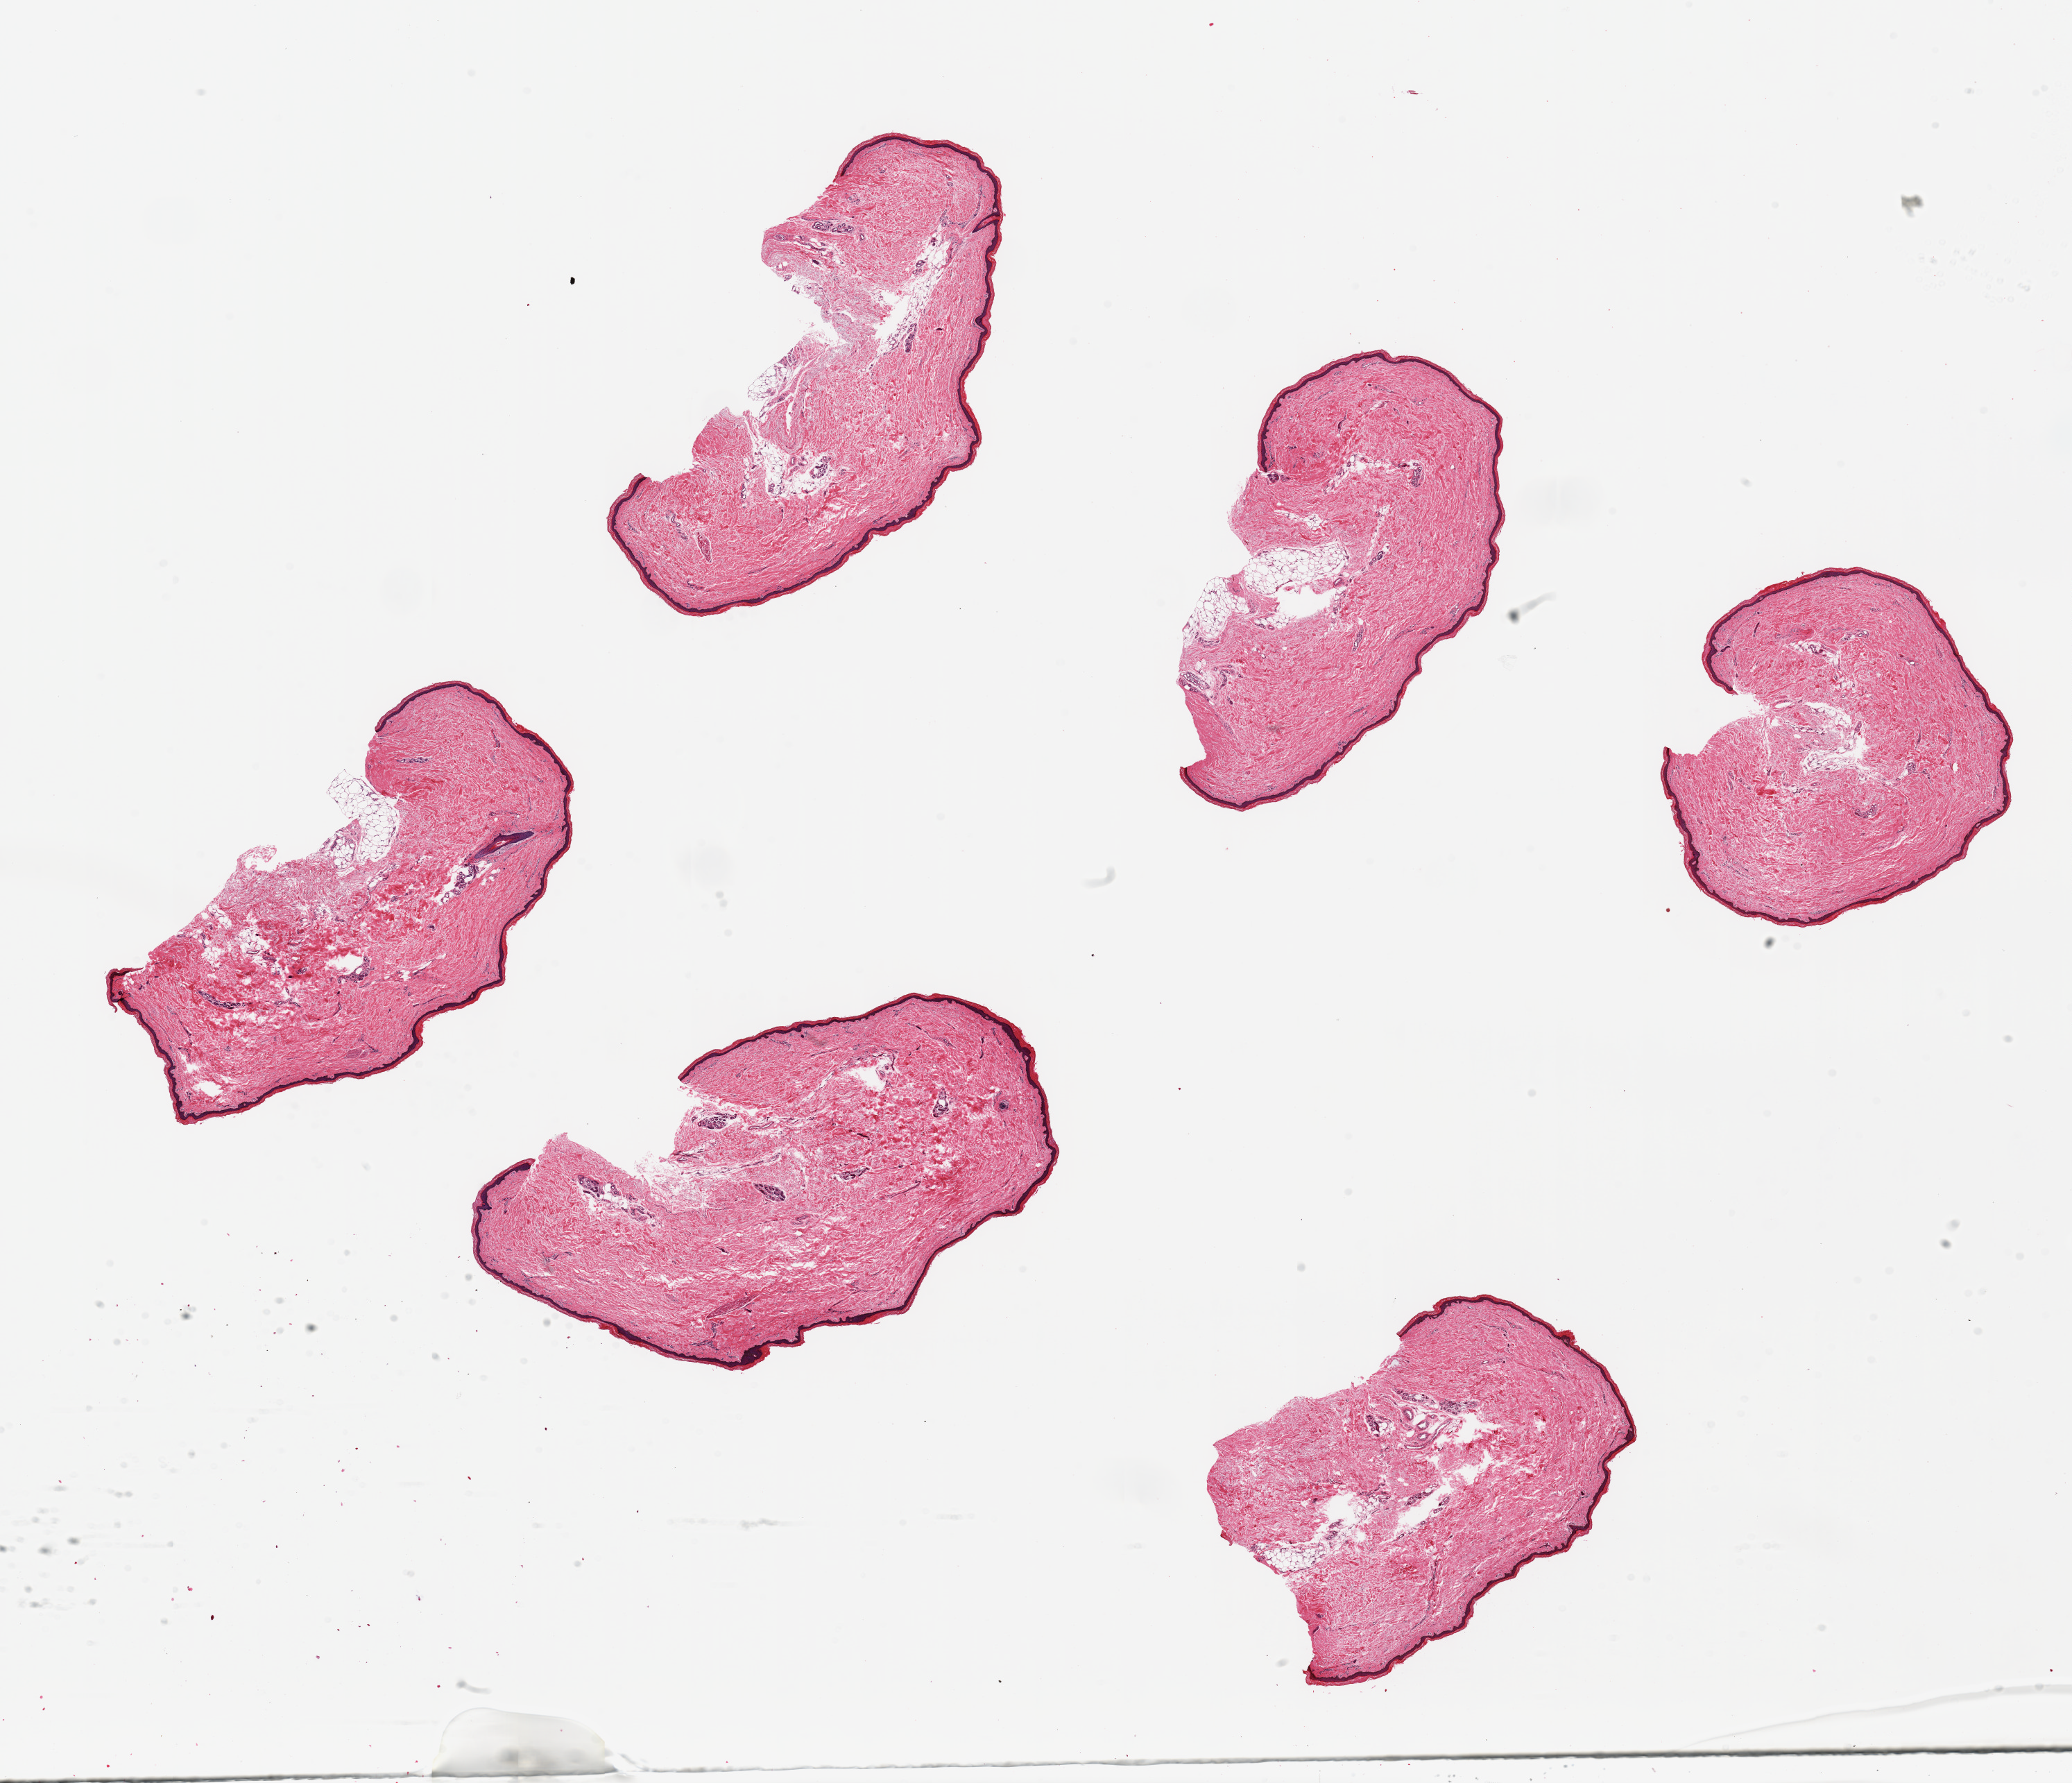
Whole-slide image, haematoxylin and eosin stain, shown as a low-resolution overview of the whole scanned area (about 23.6 x 20.3 mm); PAXgene-fixed paraffin-embedded (PFPE) section; sampled site (target tissue): skin of lower leg; donor tissue sample. Female donor.
• reviewer comment on this tissue sample: 6 pieces. up to 6x3mm; free of subcutaneous adipose